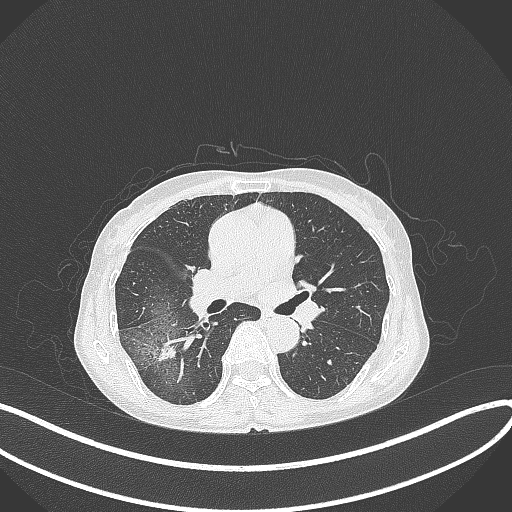
Chest CT, one axial slice; position 221 of 371 along the scan axis; reconstruction kernel B70f; 120 kVp; lung window (W 1500 / L -600 HU); 1 mm slice thickness; 512 × 512 image matrix. Female patient, age 69 years. Case-level facts recorded for this patient, not image findings: clinical TNM (as recorded): T1b N0 M0; histopathological grade: G2-3.
Outlined on this slice (rectangle marked by the reading radiologist):
- lung tumour (recorded histology: adenocarcinoma): bounding box <153,338,177,364> (left, top, right, bottom; pixels)